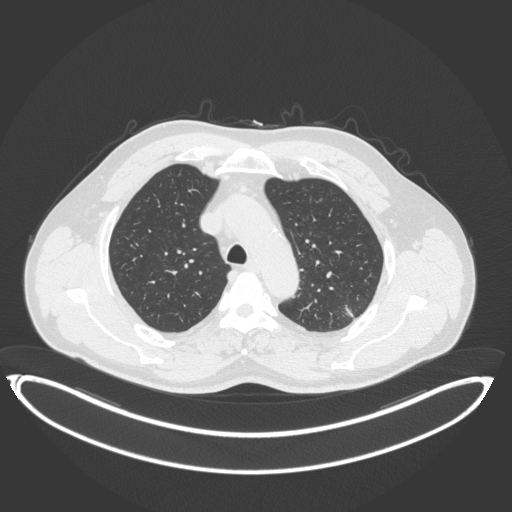
Chest CT, one axial slice; slice 276 of 399 in the series (ordered by position); 120 kVp; lung window (W 1500 / L -600 HU); 1 mm slice thickness; 512 × 512 image matrix, field of view 469 × 469 mm. Male patient, age 58 years. From the clinical record (not read from this slice): clinical TNM (as recorded): T1c N0 M0; histopathological grade: G1-2.
Structures marked on this image (bounding box drawn by a radiologist):
- lung tumour (recorded histology: adenocarcinoma): box from (x=342, y=301) to (x=359, y=321) px